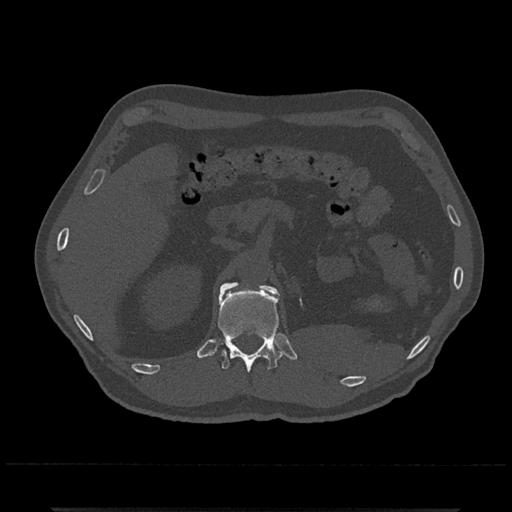
CT including the spine, one axial slice; slice 423 of 797 in the series (ordered by position); reconstruction kernel Br40s/3; 120 kVp; bone window (W 1800 / L 400 HU); 0.5 mm slice thickness; 512 × 512 image matrix. Patient: male, 67 years. From the clinical record (not read from this slice): primary cancer: prostate.
Outlined on this slice (semi-automatic segmentation, software-assisted and operator-edited):
- L1 vertebra: bounding box (x1, y1, x2, y2) in pixels: (258, 283, 276, 294)
- T12 vertebra: (217, 282, 282, 373)